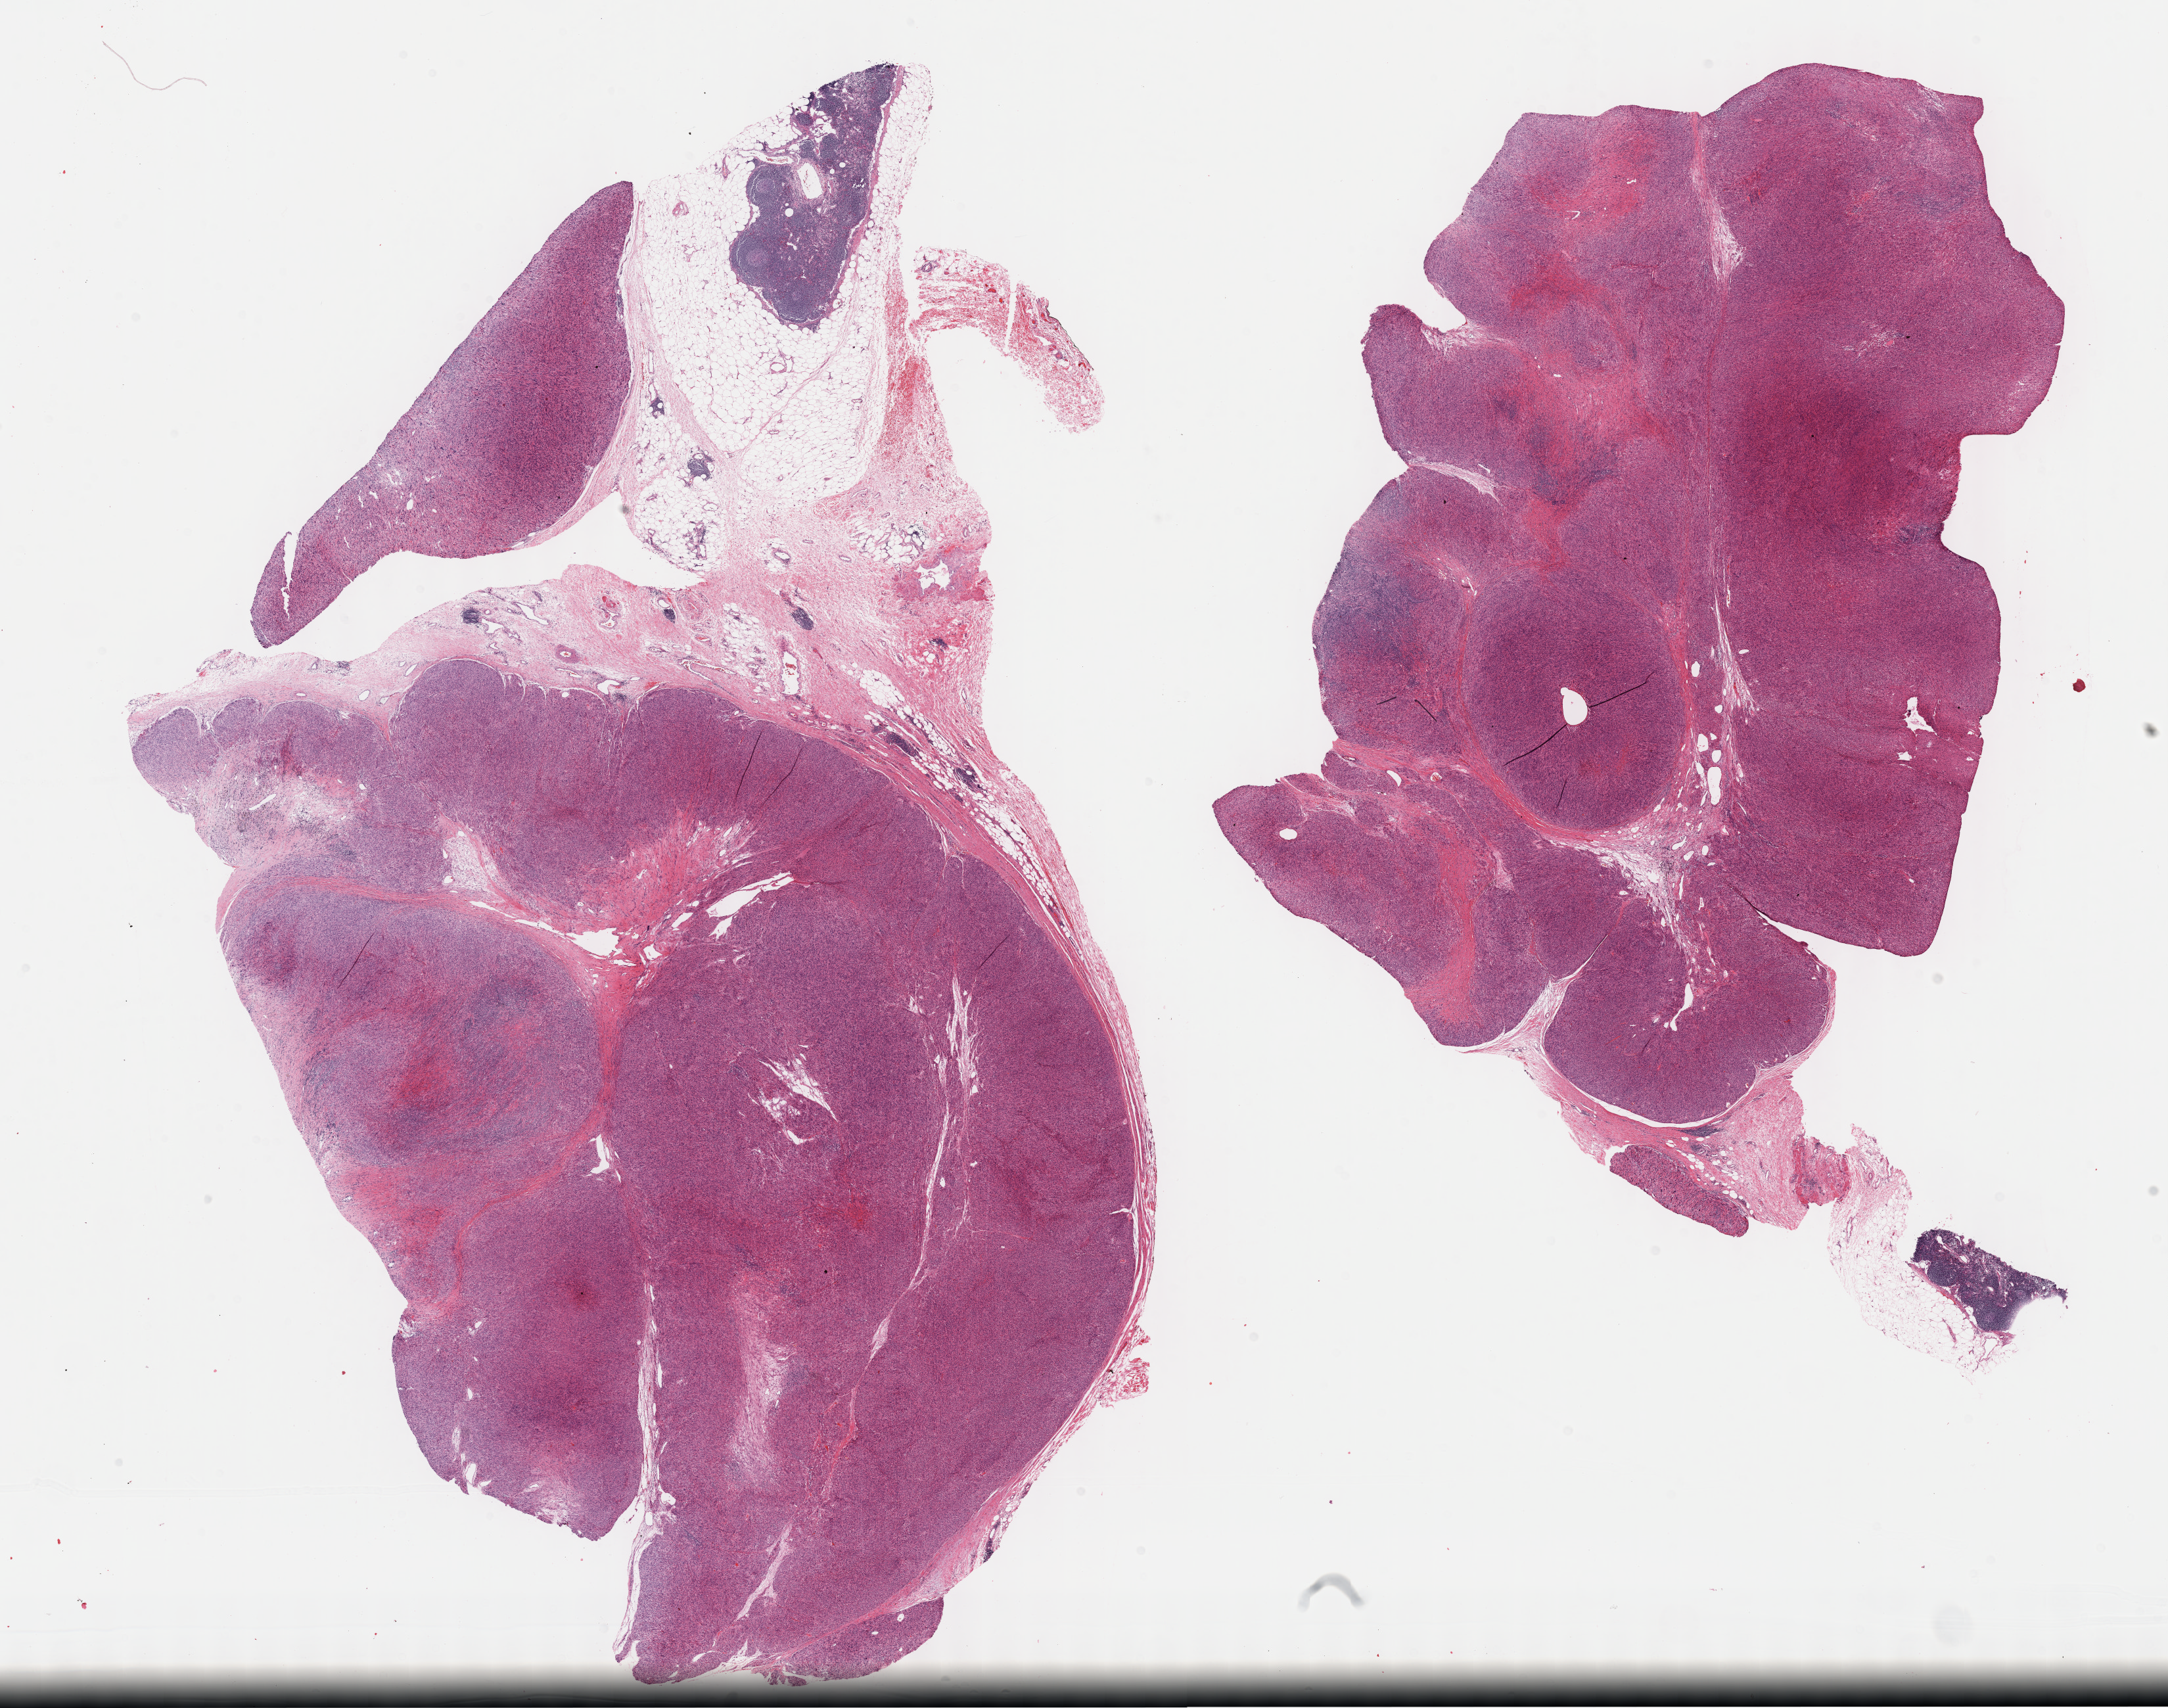
Digitized H&E tissue section (whole slide), low-resolution overview of the scanned area, about 26.7 x 21.0 mm (slide scanned at 40x). Formalin-fixed paraffin-embedded (FFPE) diagnostic section. Sample: primary tumour, retroperitoneum and peritoneum. Male patient; age at initial diagnosis 70 years.
Histologic diagnosis: Leiomyosarcoma, NOS.